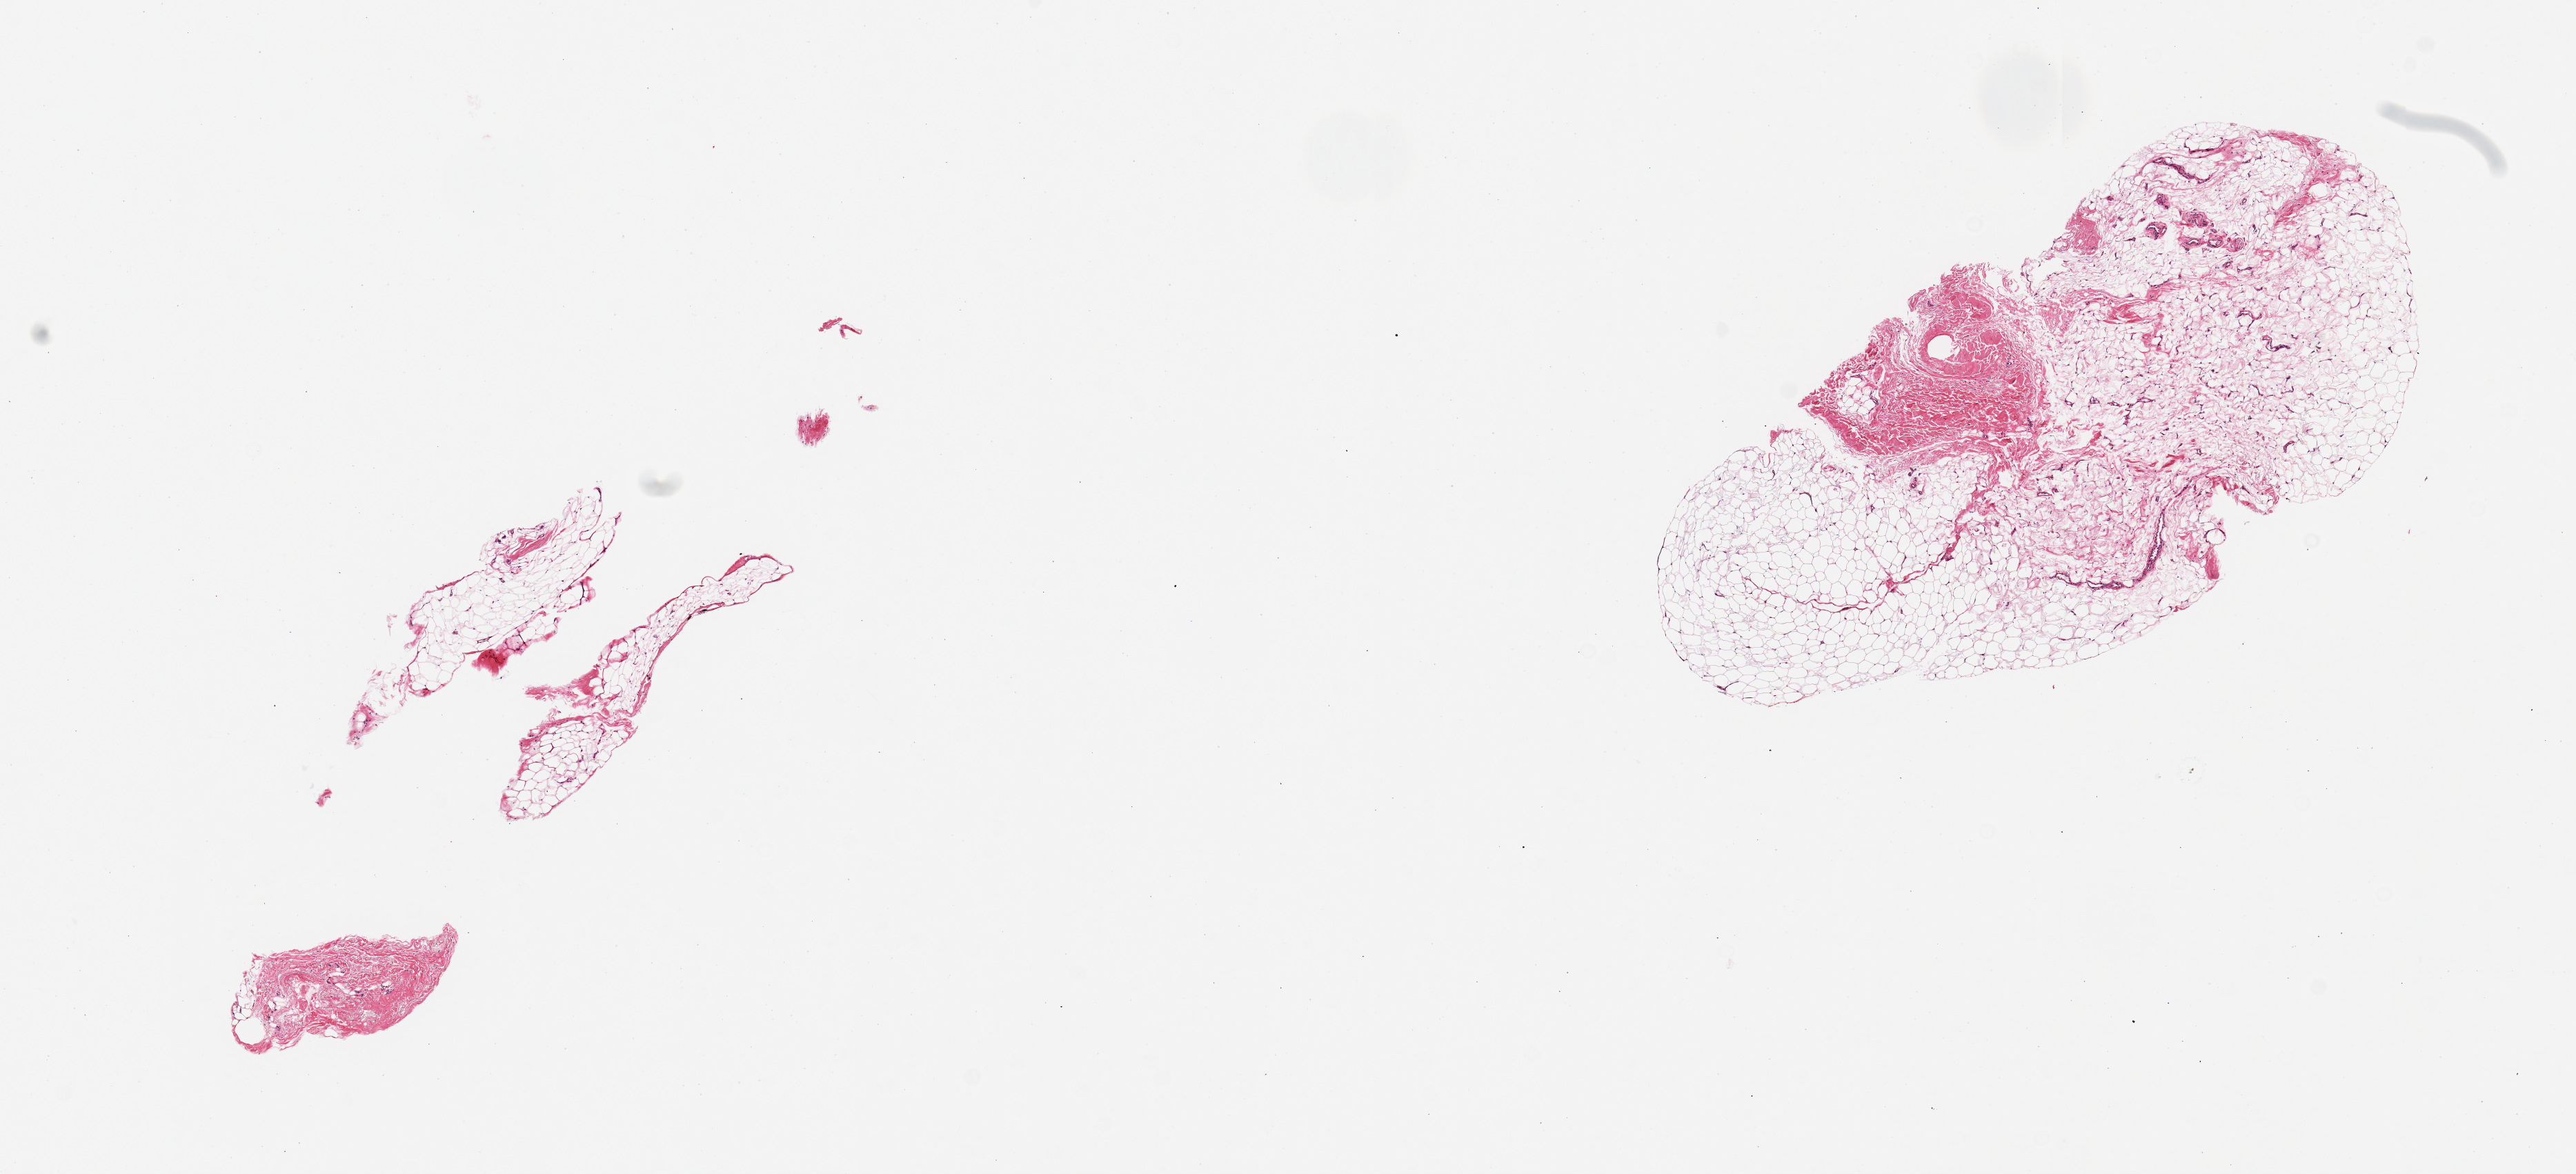
H&E whole-slide image, low-resolution overview of the scanned area, about 14.8 x 6.7 mm (slide scanned at 20x); PAXgene-fixed, paraffin-embedded tissue; sampled site (target tissue): tibial nerve; donor tissue sample. Donor sex: male.
Reviewer comment on this tissue sample: 2 pieces; fat and fibrous tissue, not nerve.